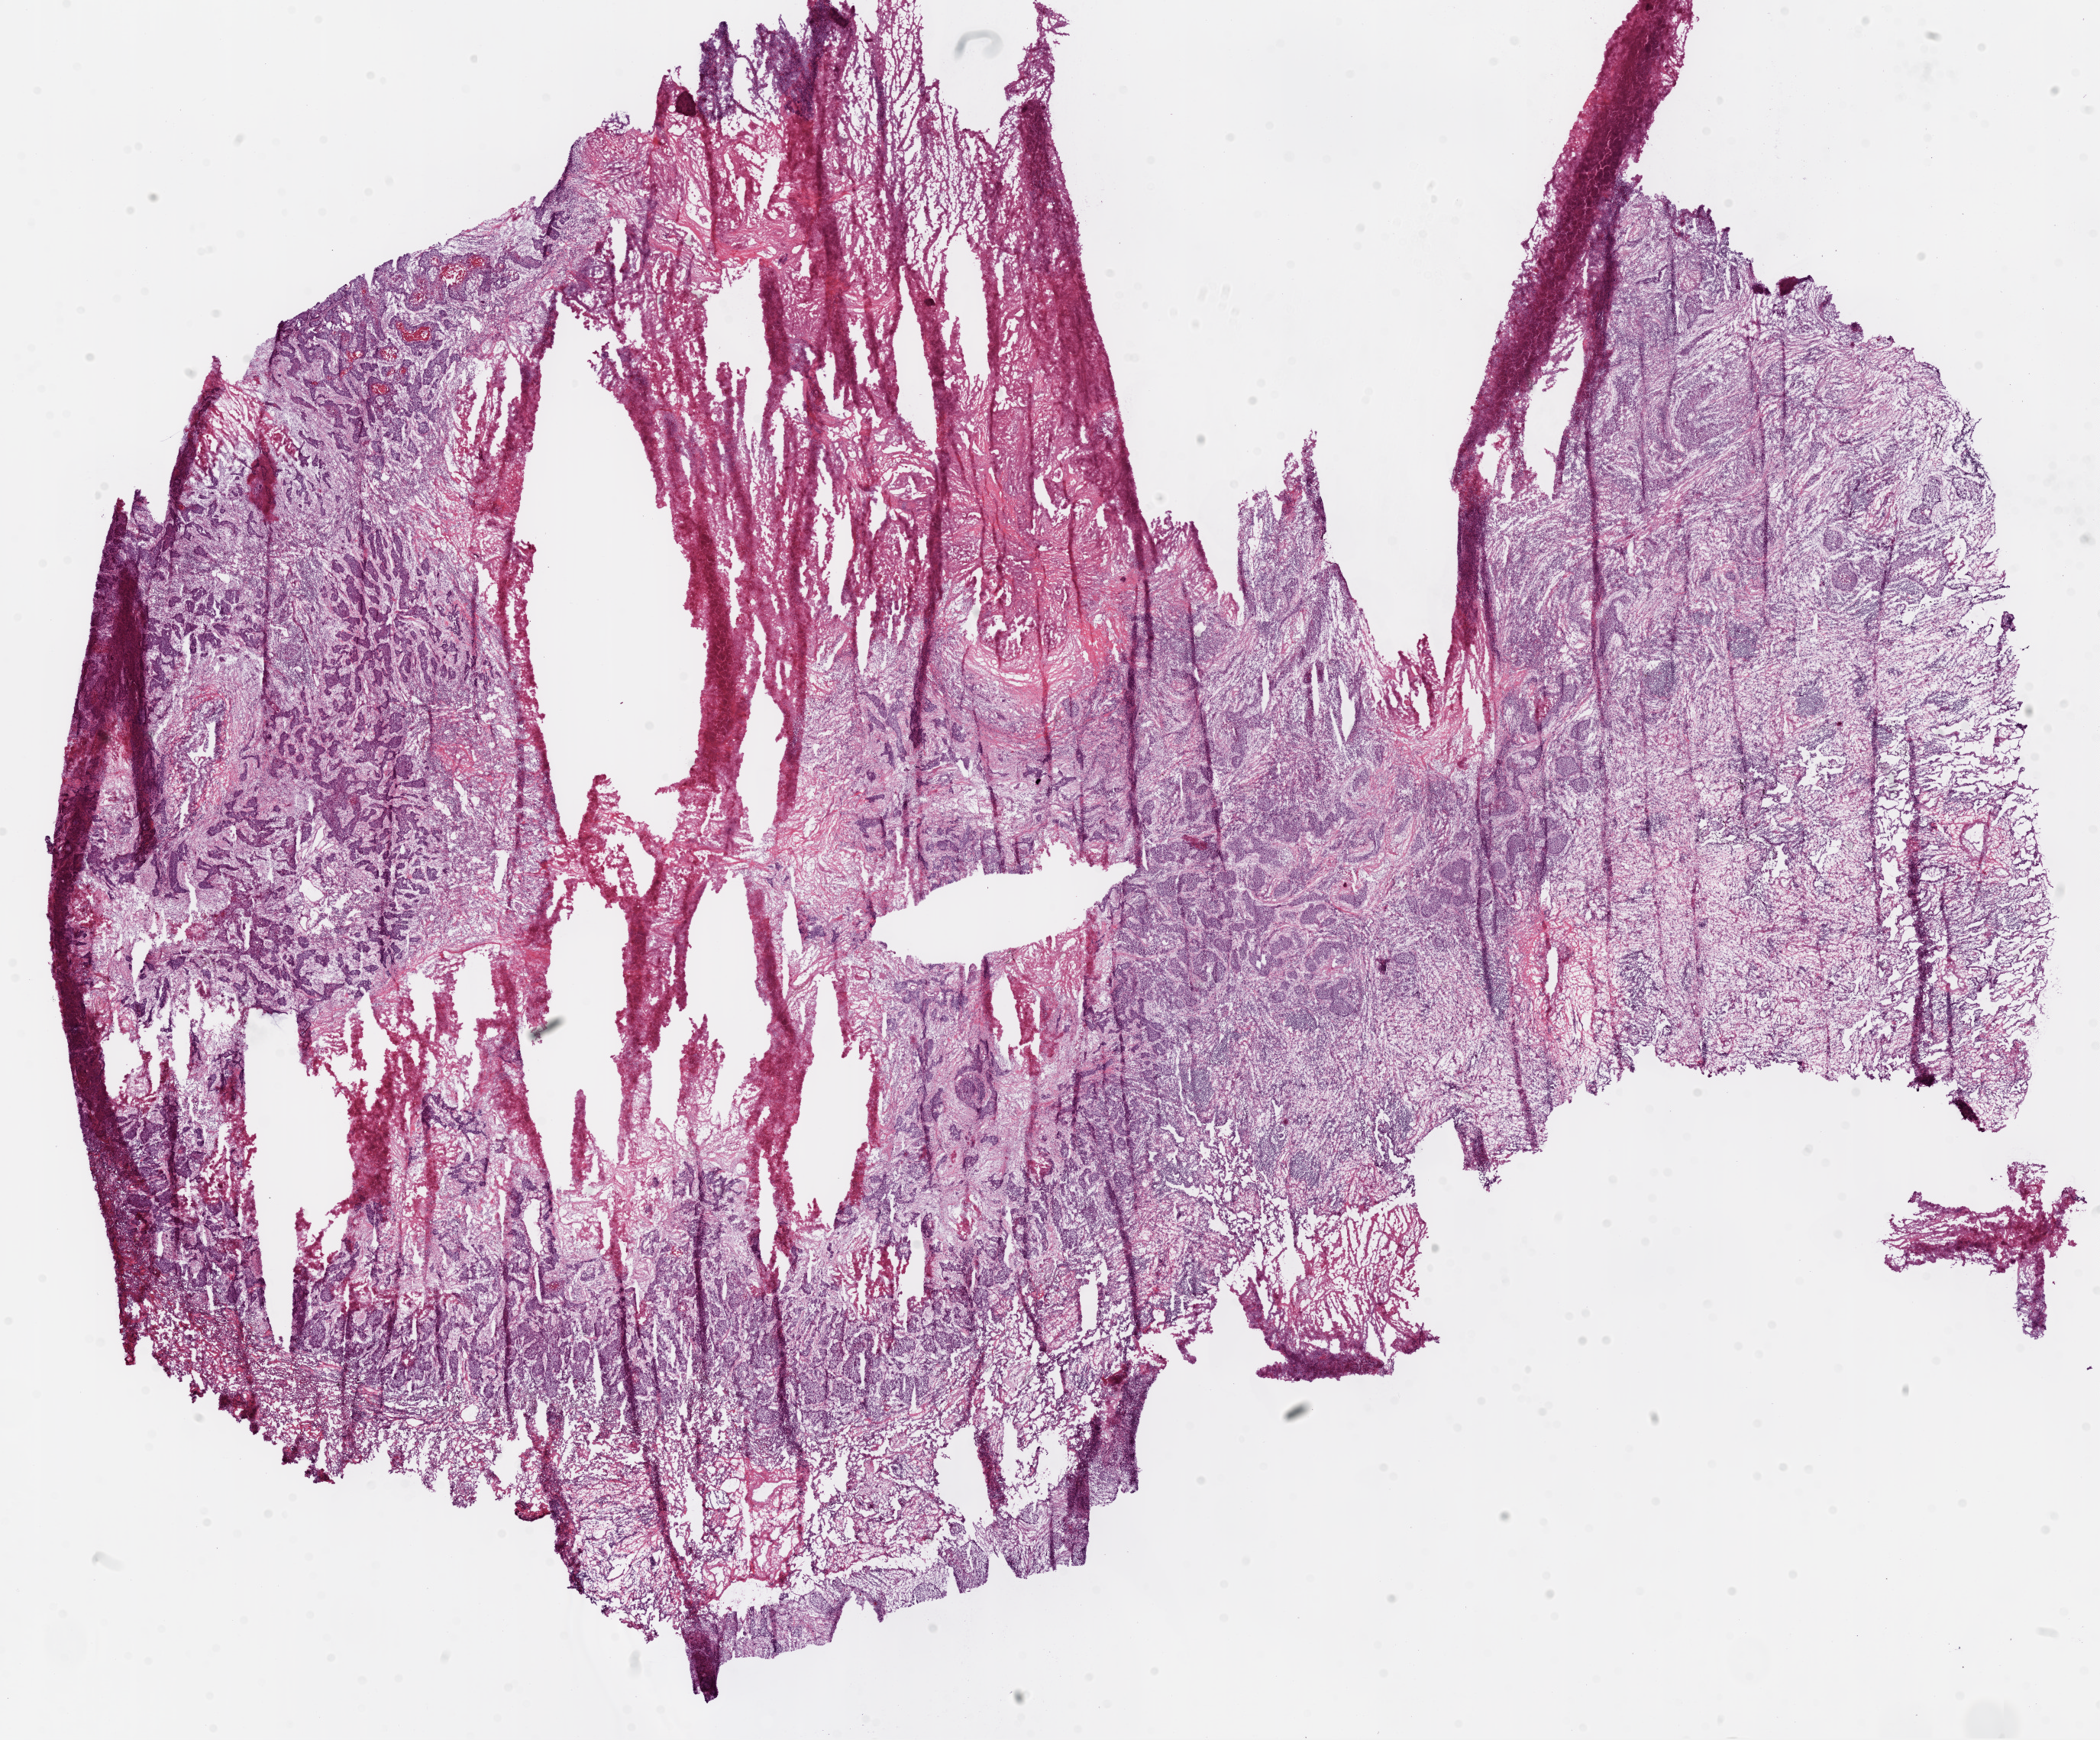
H&E whole-slide image — whole scanned area (about 22.1 x 18.3 mm) shown as a low-resolution overview; frozen section from the bottom of the tissue portion; sample: primary tumour, lung. Male patient; age at initial diagnosis 73 years. Composition of this section per pathologist review: tumour cells 62%, tumour nuclei 60%, normal cells 2%, stromal cells 15%, necrosis 20%.
• diagnosis: Squamous cell carcinoma, NOS (upper lobe, lung)
• AJCC pathologic stage: IIB (6th edition)